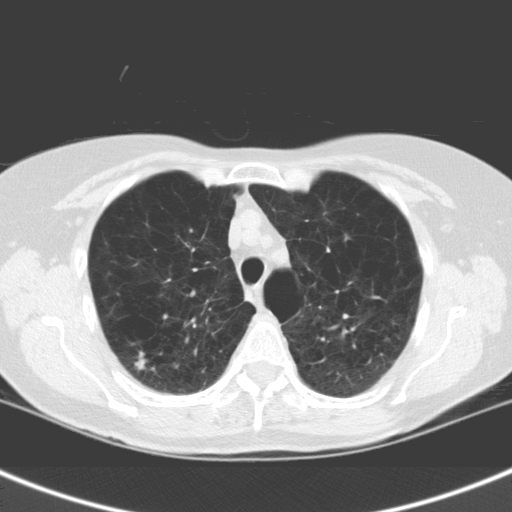
Low-dose screening chest CT, one axial slice; position 118 of 158 along the scan axis; 120 kVp; lung window (W 1500 / L -600 HU); 3.2 mm slice thickness; 512 × 512 image matrix, field of view 301 × 301 mm.
Structures marked on this image (expert manual segmentation):
- lesion 1 (tumor, upper lobe of right lung): bounding box <135,358,146,370> (left, top, right, bottom; pixels)